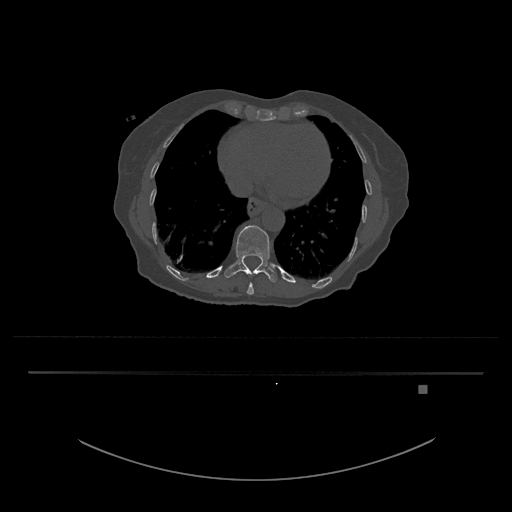
CT including the spine, one axial slice. Position 677 of 797 along the scan axis. Reconstruction kernel Br40s/3. Bone window (W 1800 / L 400 HU). 0.5 mm slice thickness. 512 × 512 image matrix, field of view 500 × 500 mm. Patient: female, 57 years. Case-level facts recorded for this patient, not image findings: primary cancer: cervical.
Outlined on this slice (semi-automatically segmented with operator editing):
- T10 vertebra: box from (x=247, y=273) to (x=255, y=295) px
- T11 vertebra: (x=224, y=225)–(x=278, y=282)